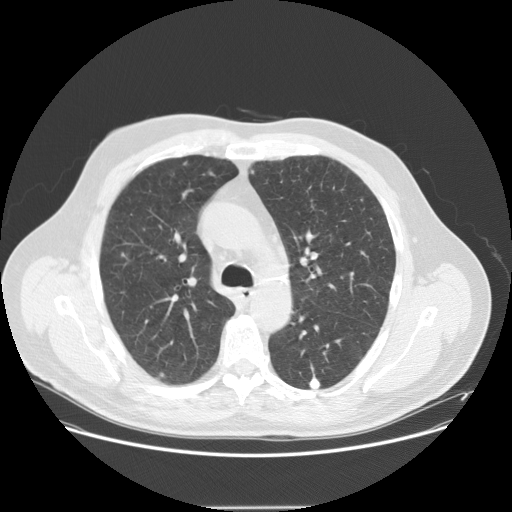
Low-dose screening chest CT, one axial slice; position 99 of 143 along the scan axis; reconstruction kernel STANDARD; lung window (W 1500 / L -600 HU); 2.5 mm slice thickness; 512 × 512 image matrix, field of view 400 × 400 mm.
Outlined on this slice (manually delineated by an expert):
- lesion 2 (tumor): box from (x=310, y=376) to (x=321, y=388) px
- lesion 6 (tumor, lower lobe of right lung): (x=158, y=373)–(x=164, y=379)